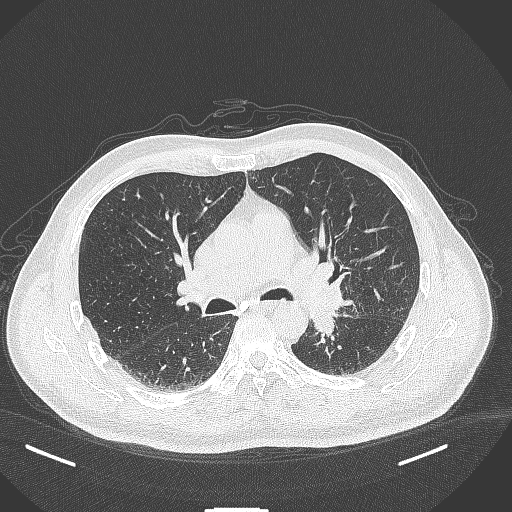
Chest CT, one axial slice. Position 249 of 429 along the scan axis. Lung window (W 1500 / L -600 HU). 1 mm slice thickness. 512 × 512 image matrix, field of view 400 × 400 mm. Patient: male, 55 years. Case-level facts recorded for this patient, not image findings: clinical TNM (as recorded): T3 N0 M1c.
Annotated regions visible in this slice (rectangle marked by the reading radiologist):
- lung tumour (recorded histology: adenocarcinoma): bounding box <308,307,342,343> (left, top, right, bottom; pixels)